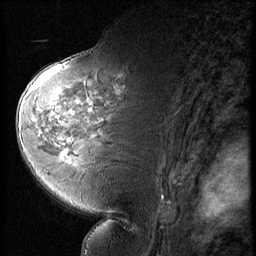
Breast MRI (dynamic contrast-enhanced), one sagittal slice. Slice 33 of 56 in the series (ordered by position). 3 images stored at this slice position (order not interpretable as contrast timing). 1.5 T. TE 4.2 ms, TR 9 ms. 2.5 mm slice thickness. 256 × 256 image matrix, field of view 180 × 180 mm. Patient: female, 58 years. From the clinical record (not read from this slice): setting: breast cancer imaged before/during neoadjuvant chemotherapy; receptor status: HR-positive, HER2-negative.
Structures marked on this image (semi-automatically segmented with operator editing):
- analysis volume of interest (the breast-tissue region the enhancement analysis was run in; not a lesion): bounding box (x1, y1, x2, y2) in pixels: (47, 136, 88, 178)
- tumour enhancement mask (voxels above the 140 % enhancement threshold inside the analysis volume of interest): (60, 150, 71, 162)